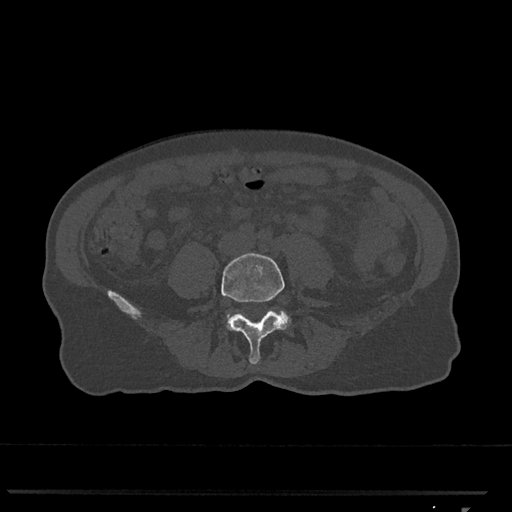
CT including the spine, one axial slice. Slice 197 of 793 in the series (ordered by position). 120 kVp. Bone window (W 1800 / L 400 HU). 512 × 512 image matrix. Patient: female, 62 years. From the clinical record (not read from this slice): primary cancer: renal.
Structures marked on this image (semi-automatic segmentation, software-assisted and operator-edited):
- L4 vertebra: box from (x=221, y=253) to (x=286, y=365) px
- L5 vertebra: (x=227, y=311)–(x=291, y=325)